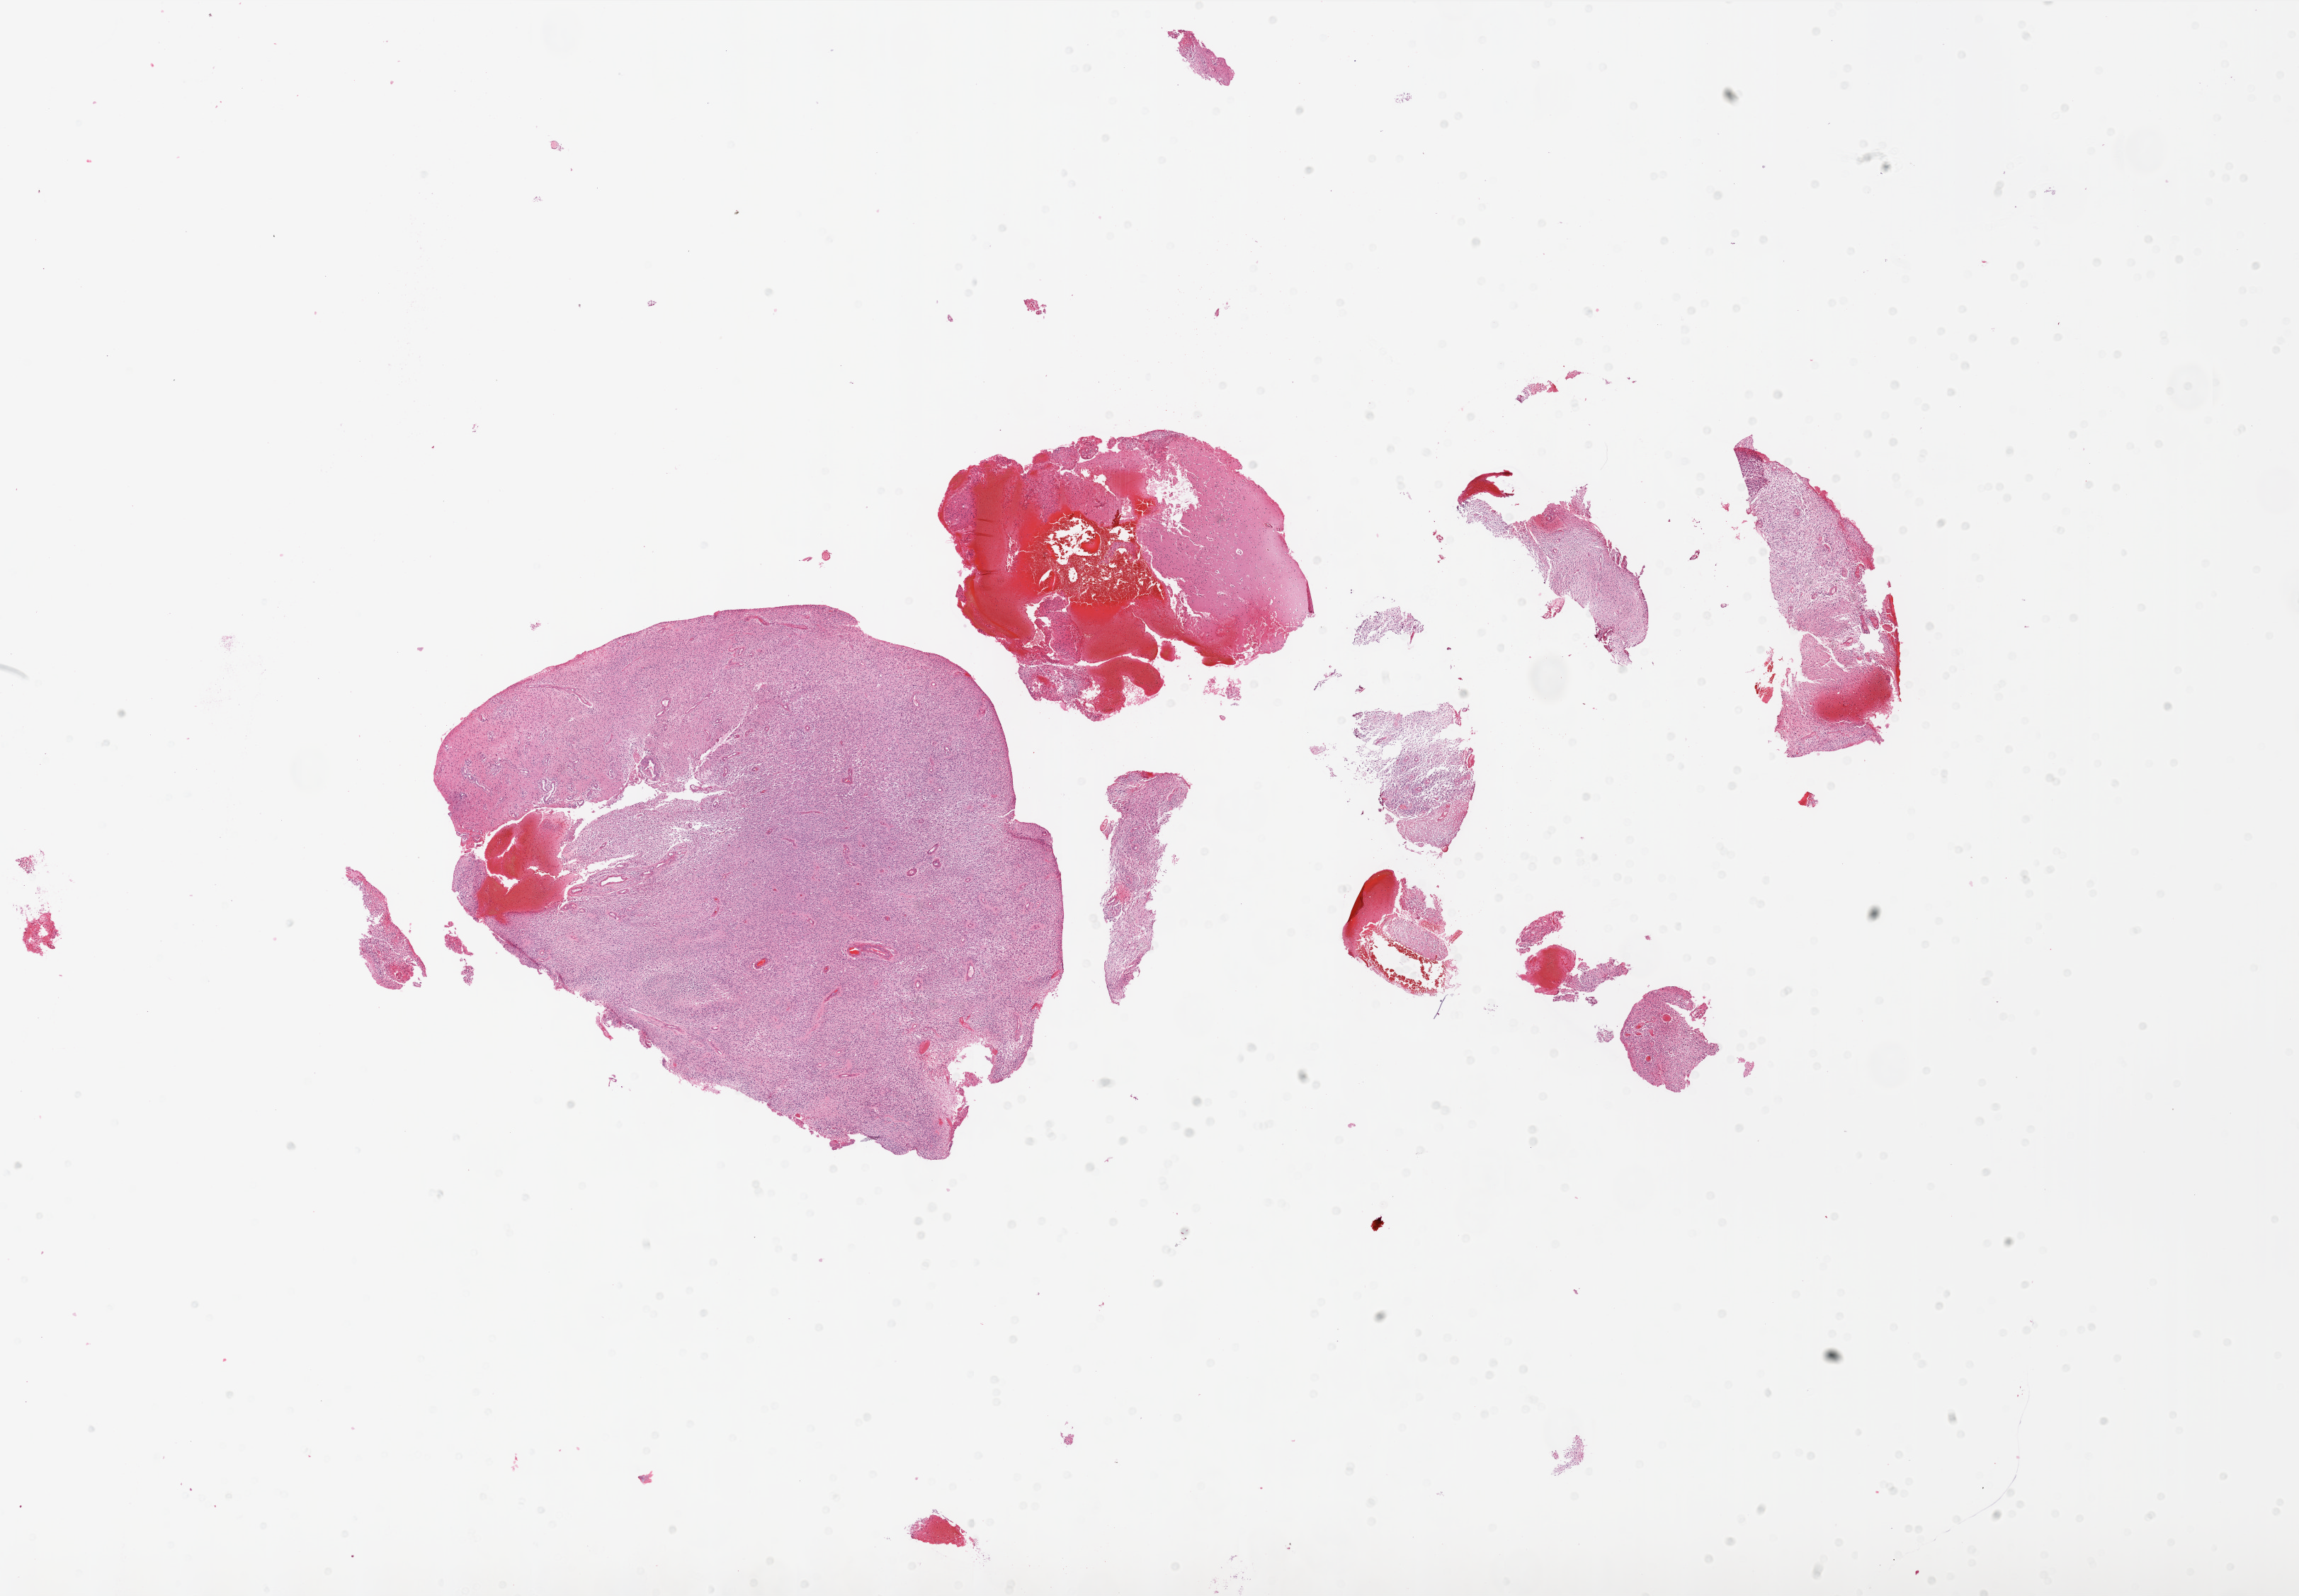
Digitized H&E tissue section (whole slide) — a low-resolution overview of the entire scanned area, about 26.0 x 18.0 mm (slide scanned at 20x). Formalin-fixed paraffin-embedded (FFPE) diagnostic section. Primary tumour sample from the brain. Female, age 72 years at initial diagnosis.
* pathologic diagnosis: Glioblastoma